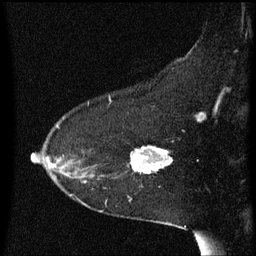
Breast MRI (dynamic contrast-enhanced), one sagittal slice. Position 42 of 60 along the scan axis. Dynamic contrast-enhanced series, image 2 of 3 at this slice position (ordered by acquisition). 1.5 T. TE 4.2 ms, TR 8.4 ms. 2 mm slice thickness. 256 × 256 image matrix. Female patient, age 54 years. Case-level facts recorded for this patient, not image findings: setting: breast cancer imaged before/during neoadjuvant chemotherapy; receptor status: HR-positive, HER2-negative.
Annotated regions visible in this slice (semi-automatically segmented with operator editing):
- analysis volume of interest (the breast-tissue region the enhancement analysis was run in; not a lesion): bounding box <117,146,174,179> (left, top, right, bottom; pixels)
- tumour enhancement mask (voxels above the 70 % enhancement threshold inside the analysis volume of interest): <132,146,173,175>